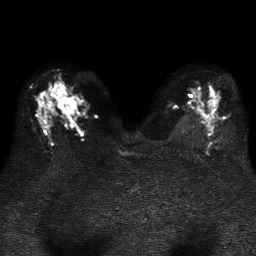
Breast MRI, one axial slice. Position 22 of 37 along the scan axis. Diffusion-weighted series; image 2 of 4 stored at this slice position (different b-values; order by instance number). 1.5 T. 5 mm slice thickness. 256 × 256 image matrix. Female patient.
Outlined on this slice (manually delineated by an expert):
- tumour on diffusion-weighted imaging: bounding box [x1, y1, x2, y2] px = [59, 97, 76, 114]